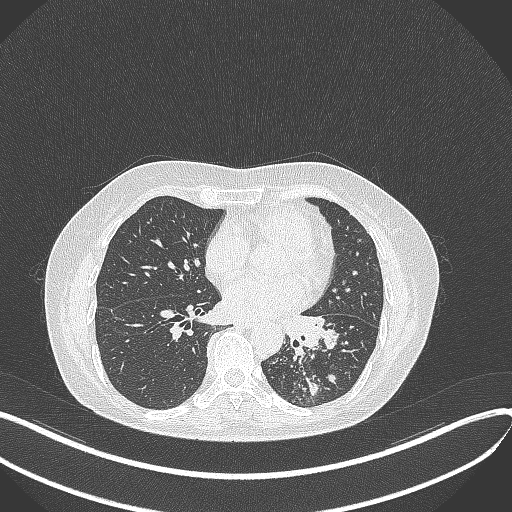
Chest CT, one axial slice; position 180 of 429 along the scan axis; reconstruction kernel B70f; 100 kVp; lung window (W 1500 / L -600 HU); 512 × 512 image matrix, field of view 400 × 400 mm. Patient: female, 63 years. Case-level facts recorded for this patient, not image findings: clinical TNM (as recorded): T1b N0 M0.
Structures marked on this image (rectangle marked by the reading radiologist):
- lung tumour (recorded histology: adenocarcinoma): bounding box <283,308,336,355> (left, top, right, bottom; pixels)